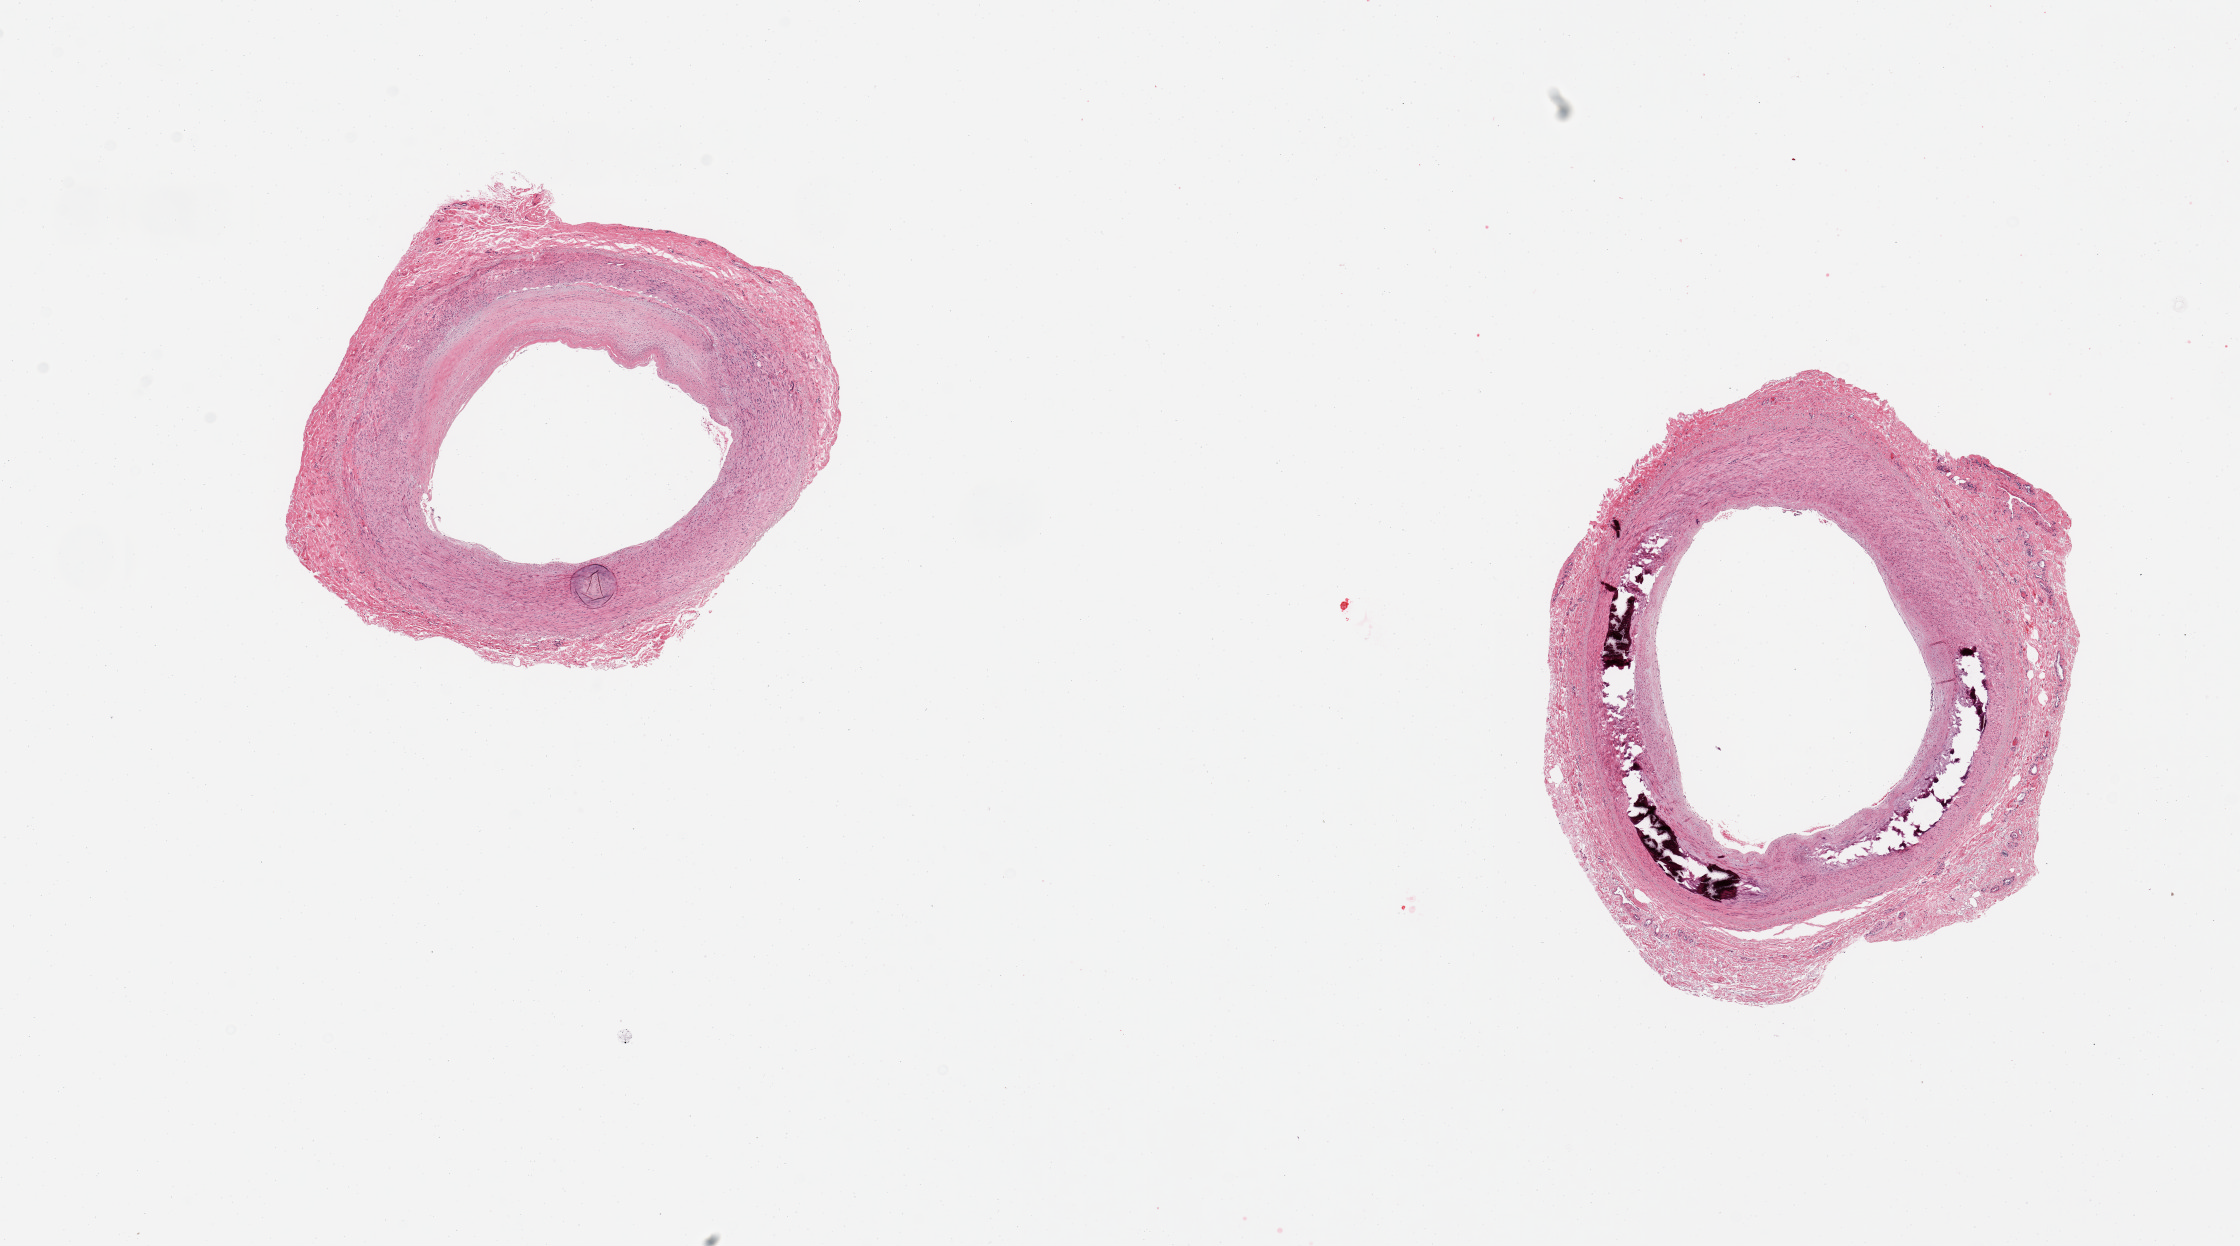
Digitized H&E-stained section — whole scanned area (about 17.7 x 9.9 mm) shown as a low-resolution overview; PAXgene-fixed paraffin-embedded (PFPE) section; section of tibial artery (target tissue); donor tissue sample. Male donor.
Reviewer comment on this tissue sample: 2 pieces, clean specimens, ~20-30% occlusive atherosis; foci of Monckeberg's sclerosis.